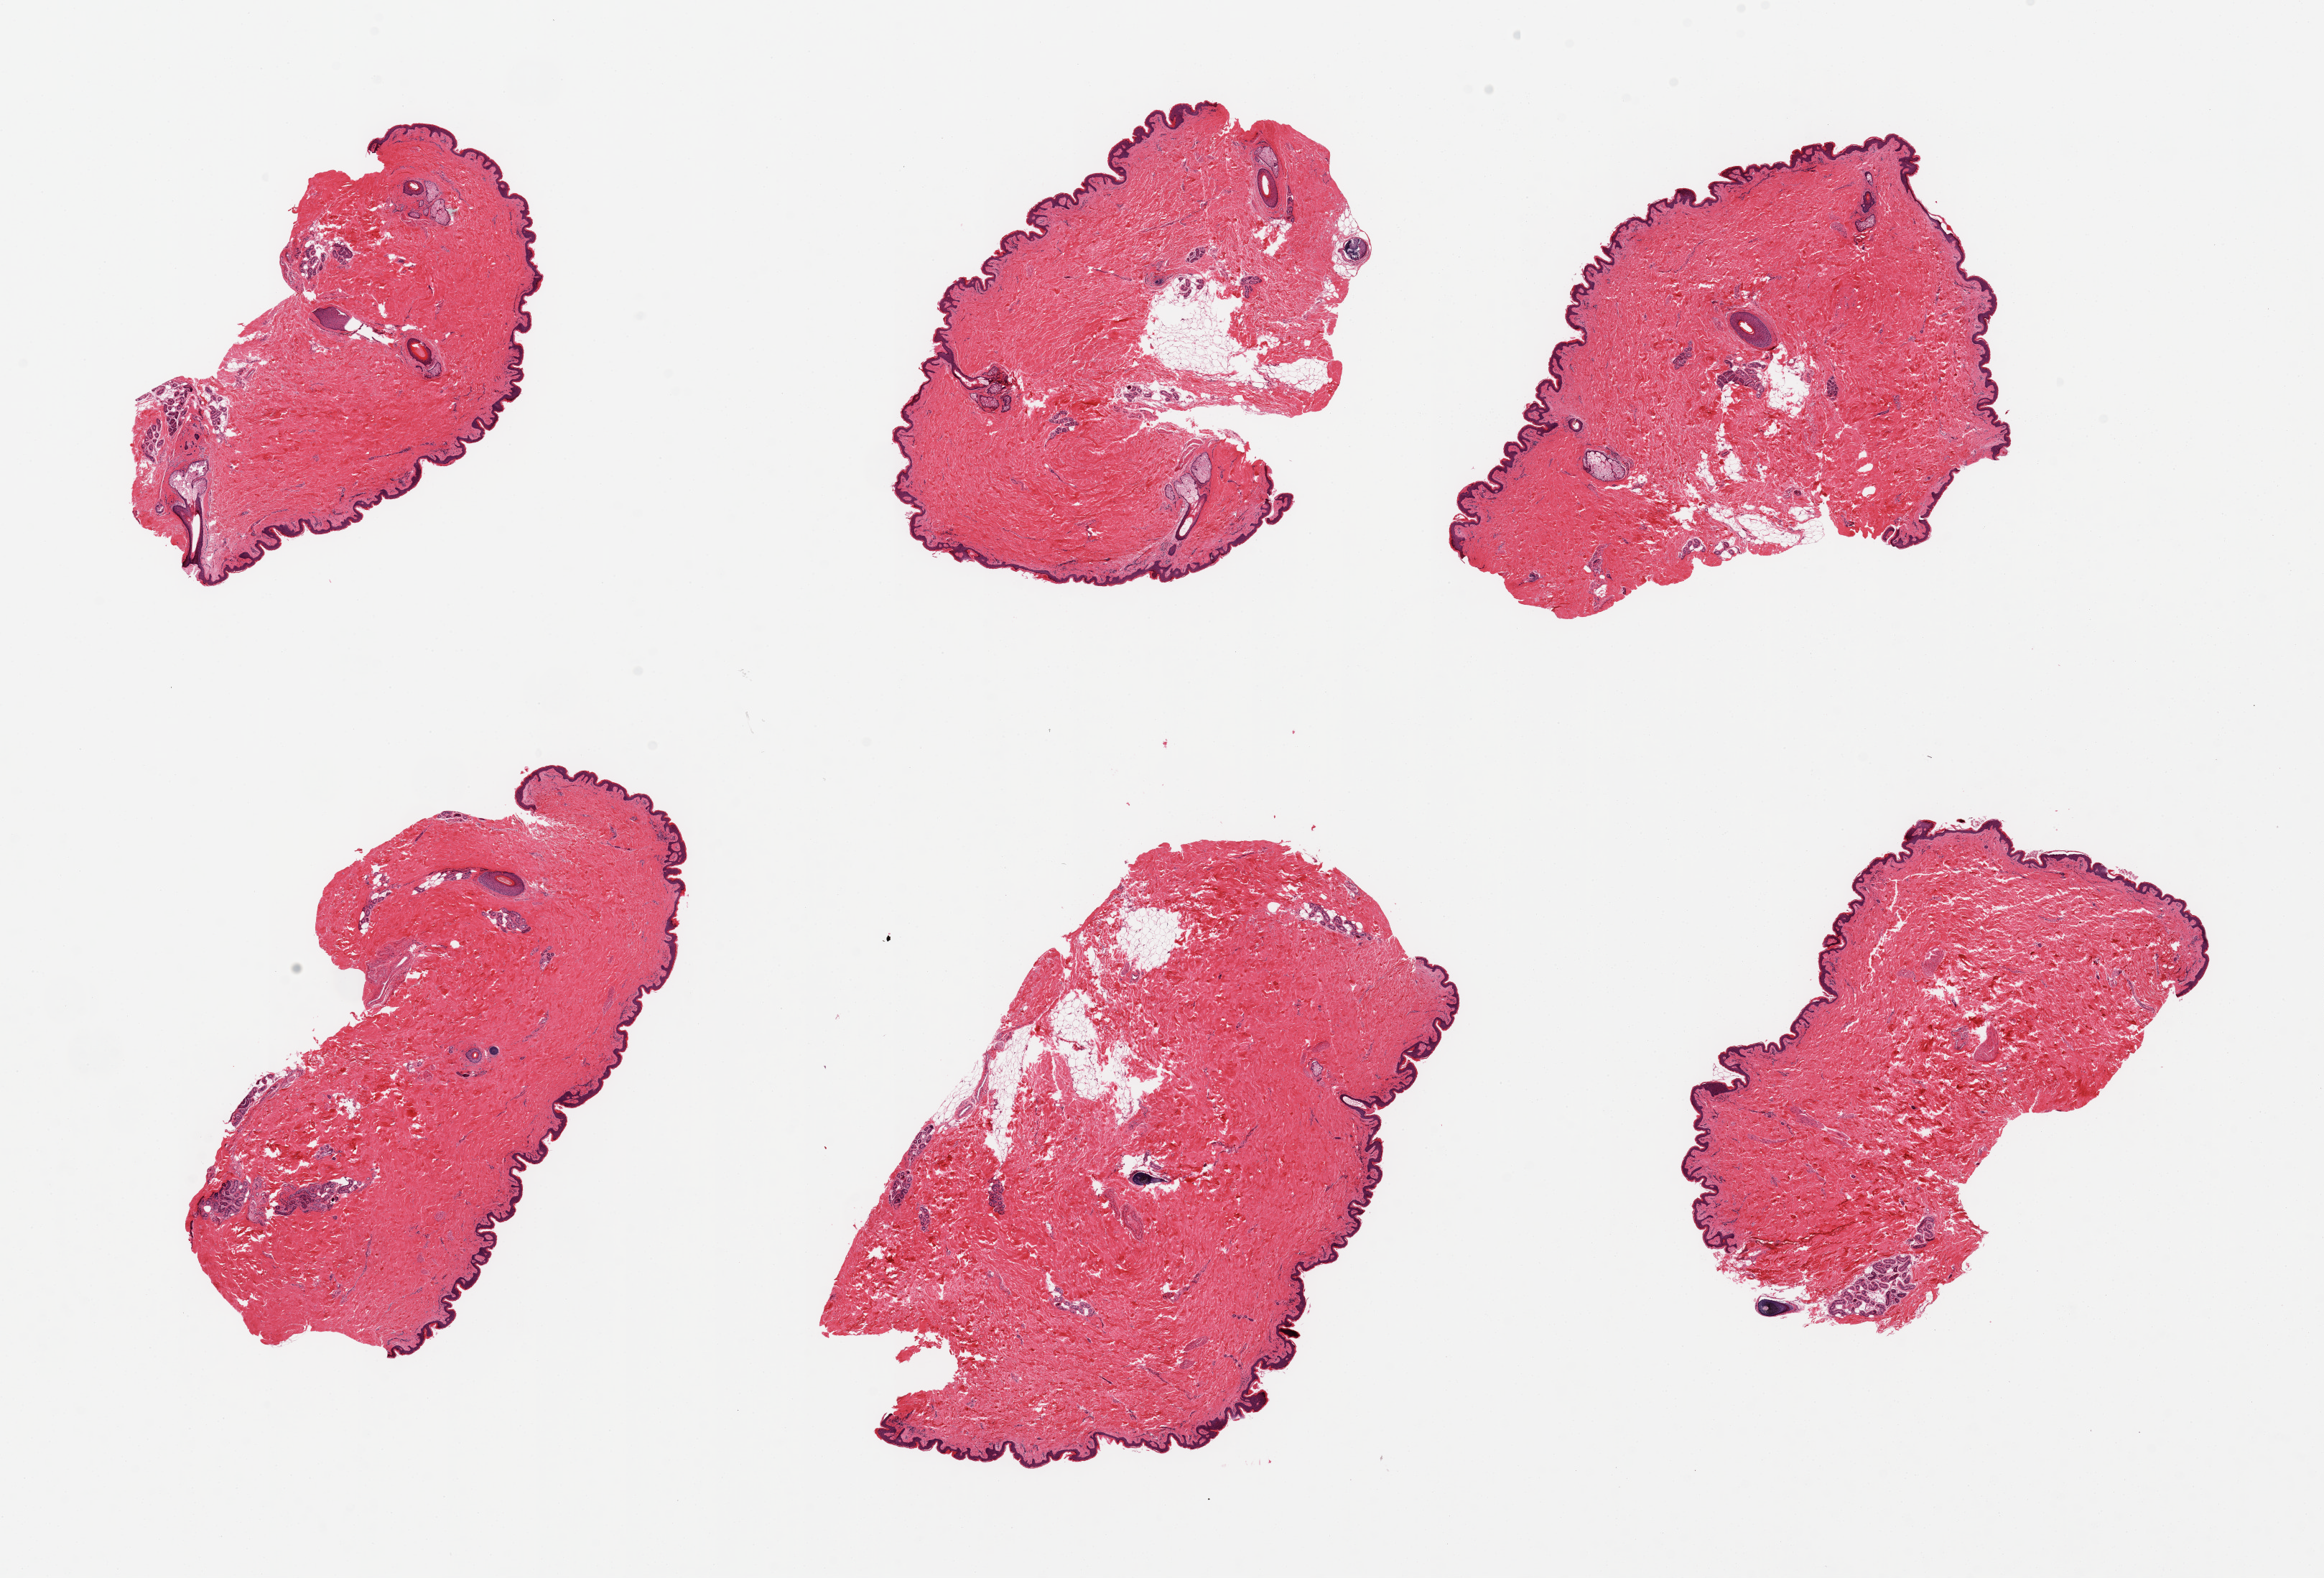
Whole-slide image, H&E stain, whole scanned area (about 25.6 x 17.4 mm) shown as a low-resolution overview, PAXgene-fixed paraffin-embedded (PFPE) section, section of skin of suprapubic region (target tissue), donor tissue sample. Male donor.
Pathologist's review note for this sample: 6 pieces squamous epithelium is ~50 microns. Minimal dermal fat.